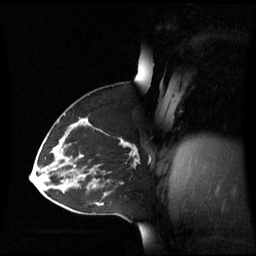
Breast MRI (dynamic contrast-enhanced), one sagittal slice. Position 36 of 60 along the scan axis. Dynamic contrast-enhanced series, image 2 of 3 at this slice position (ordered by acquisition). 1.5 T. TE 4.2 ms, TR 8.4 ms. 2.8 mm slice thickness. 256 × 256 image matrix, field of view 270 × 270 mm. Female patient, age 43 years. From the clinical record (not read from this slice): setting: breast cancer imaged before/during neoadjuvant chemotherapy; receptor status: triple-negative.
Annotated regions visible in this slice (semi-automatic segmentation, software-assisted and operator-edited):
- analysis volume of interest (the breast-tissue region the enhancement analysis was run in; not a lesion): bounding box <55,124,140,173> (left, top, right, bottom; pixels)
- tumour enhancement mask (voxels above the 70 % enhancement threshold inside the analysis volume of interest): <58,138,139,165>